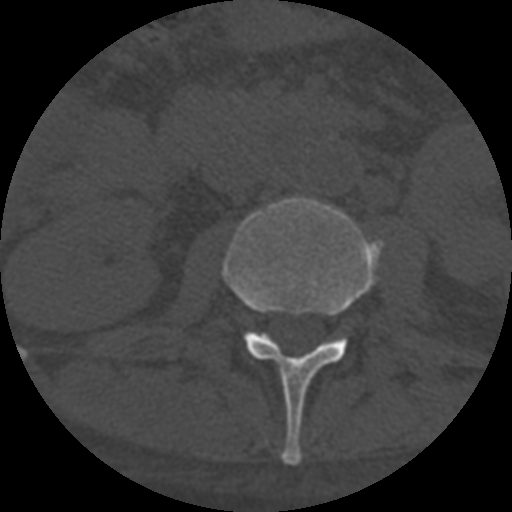
CT including the spine, one axial slice. Position 256 of 708 along the scan axis. Reconstruction kernel STANDARD. One of 3 acquisitions stored at this slice position. Bone window (W 1800 / L 400 HU). 1.25 mm slice thickness. 512 × 512 image matrix, field of view 160 × 160 mm. Patient age 55 years. Case-level facts recorded for this patient, not image findings: primary cancer: colon.
Structures marked on this image (semi-automatically segmented with operator editing):
- L2 vertebra: bounding box (x1, y1, x2, y2) in pixels: (222, 197, 383, 466)